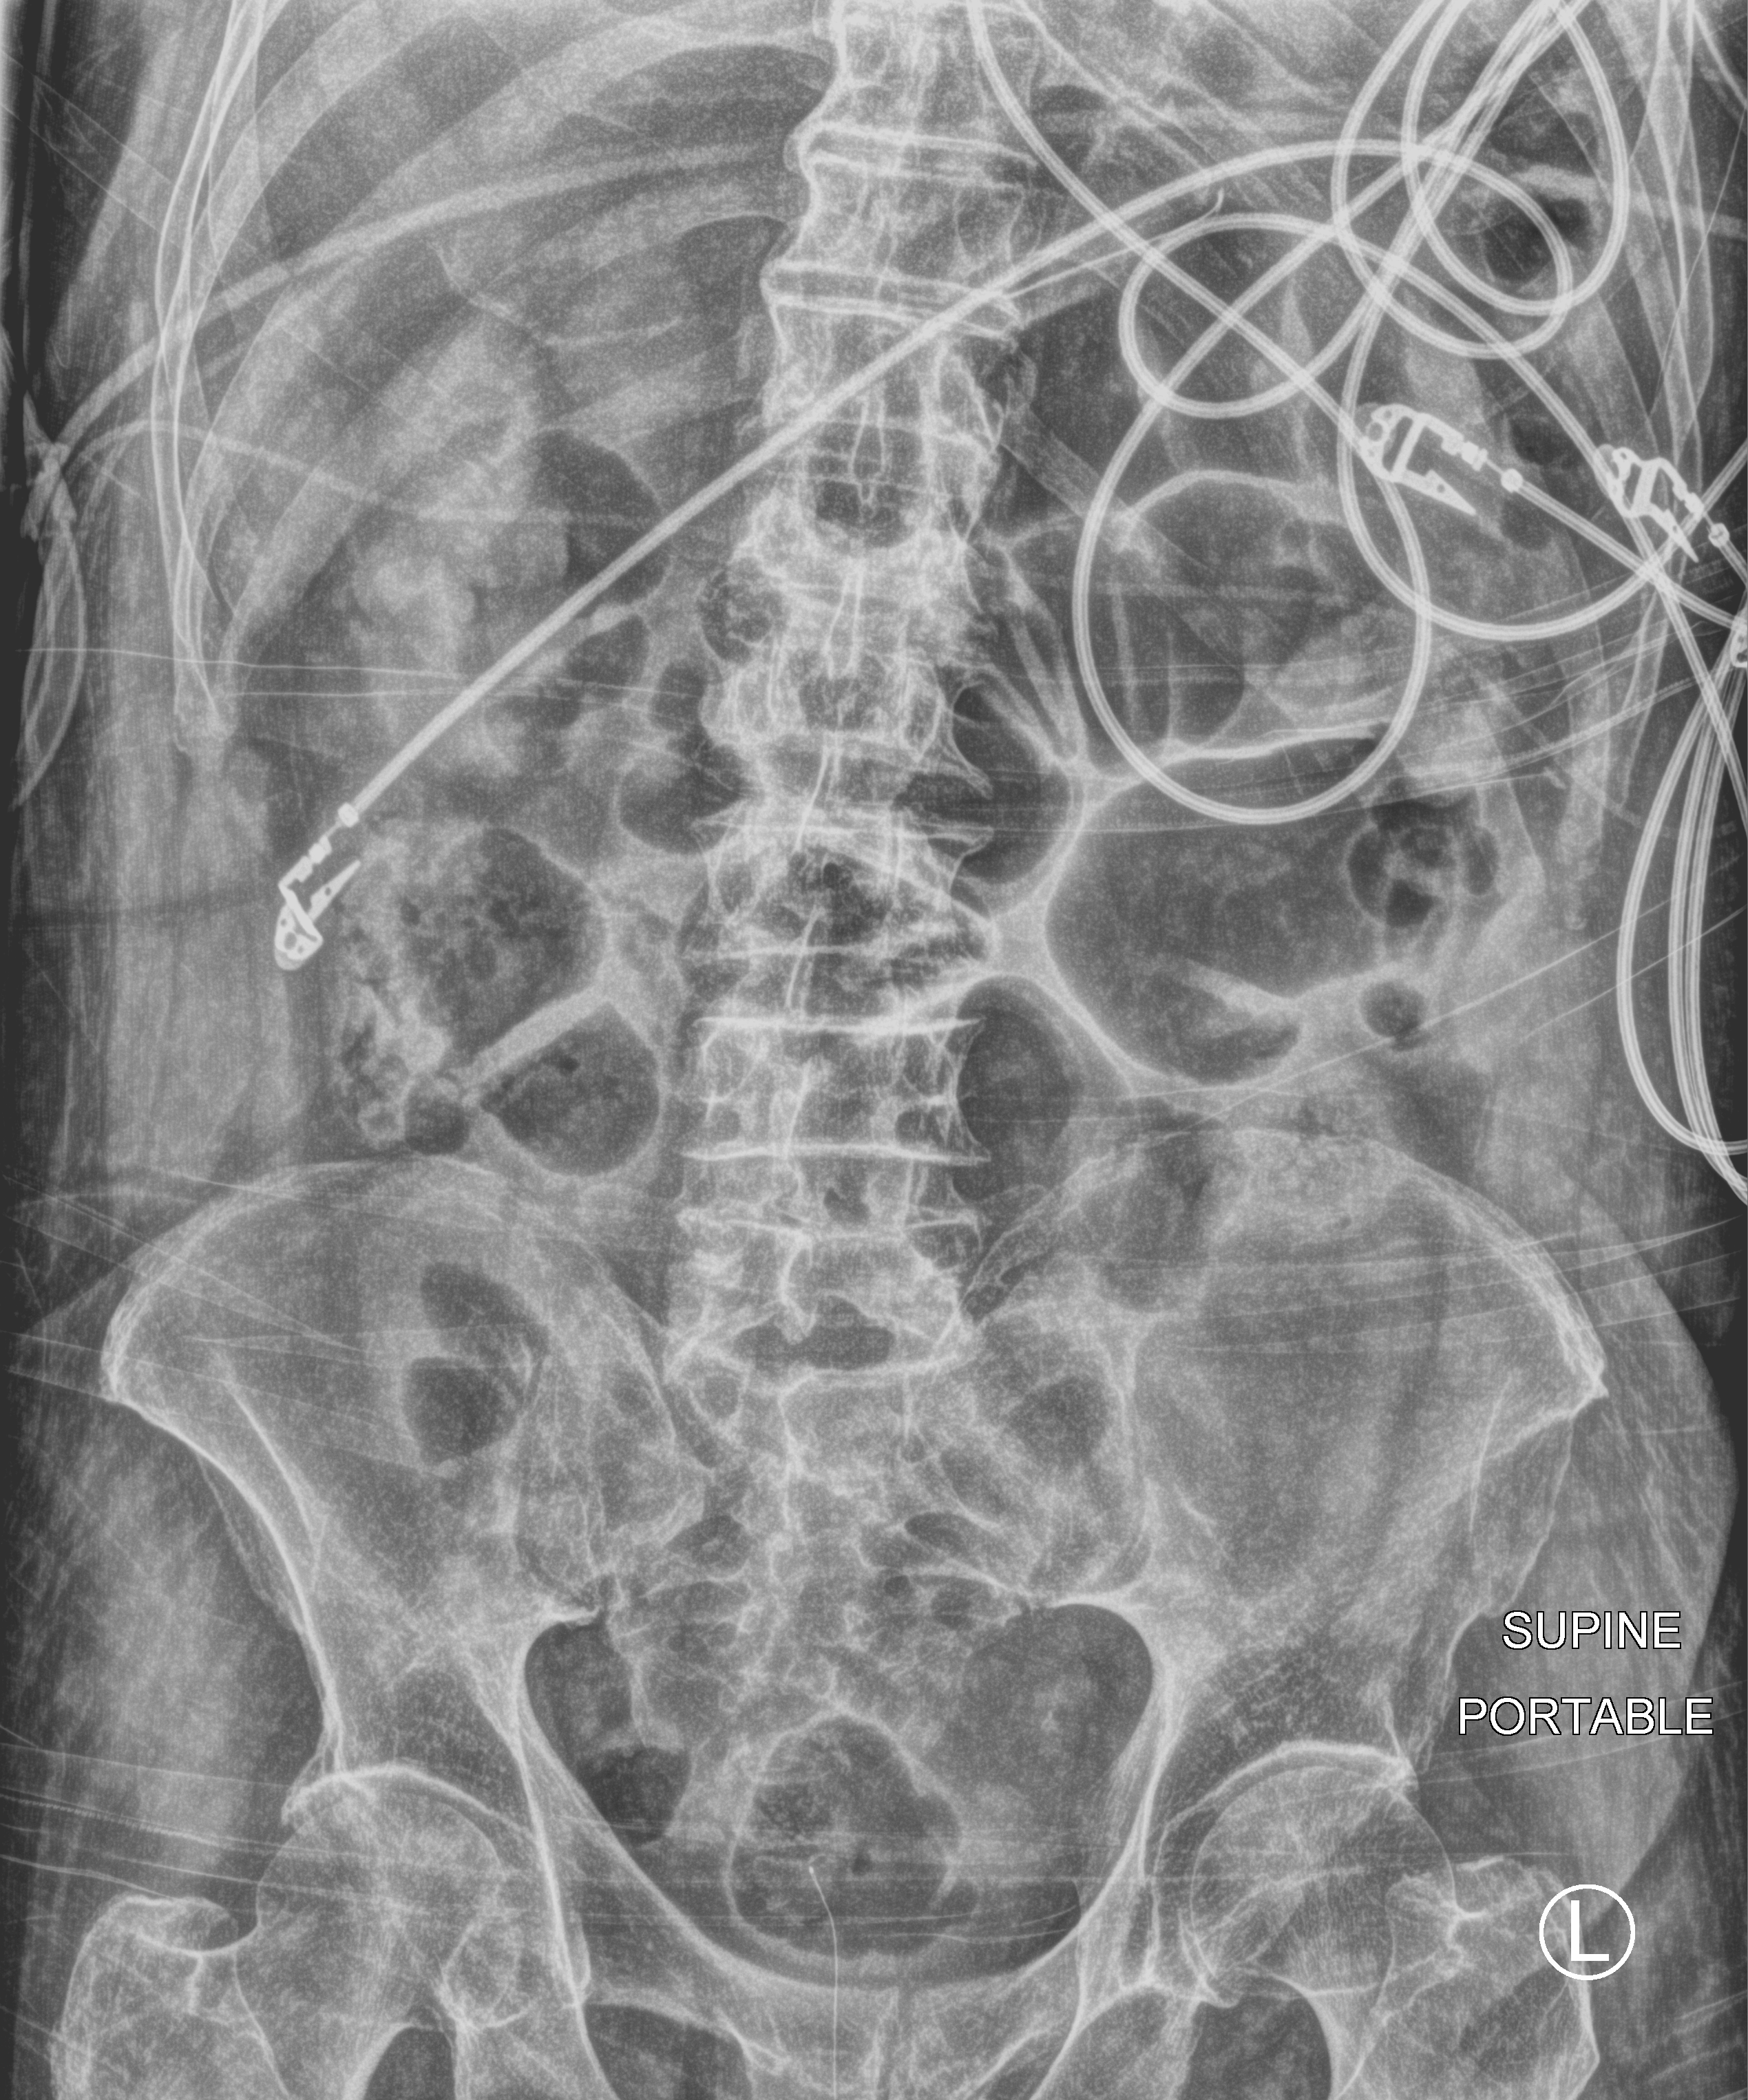
Abdomen X-ray (portable); anteroposterior (AP) projection. Patient hospitalised with COVID-19; male, aged 75–90 years.
From the hospital-stay record, not from the radiograph (when in the stay this image was taken is not recorded): mechanically ventilated during this hospital stay: yes; admitted to intensive care during this hospital stay: yes.